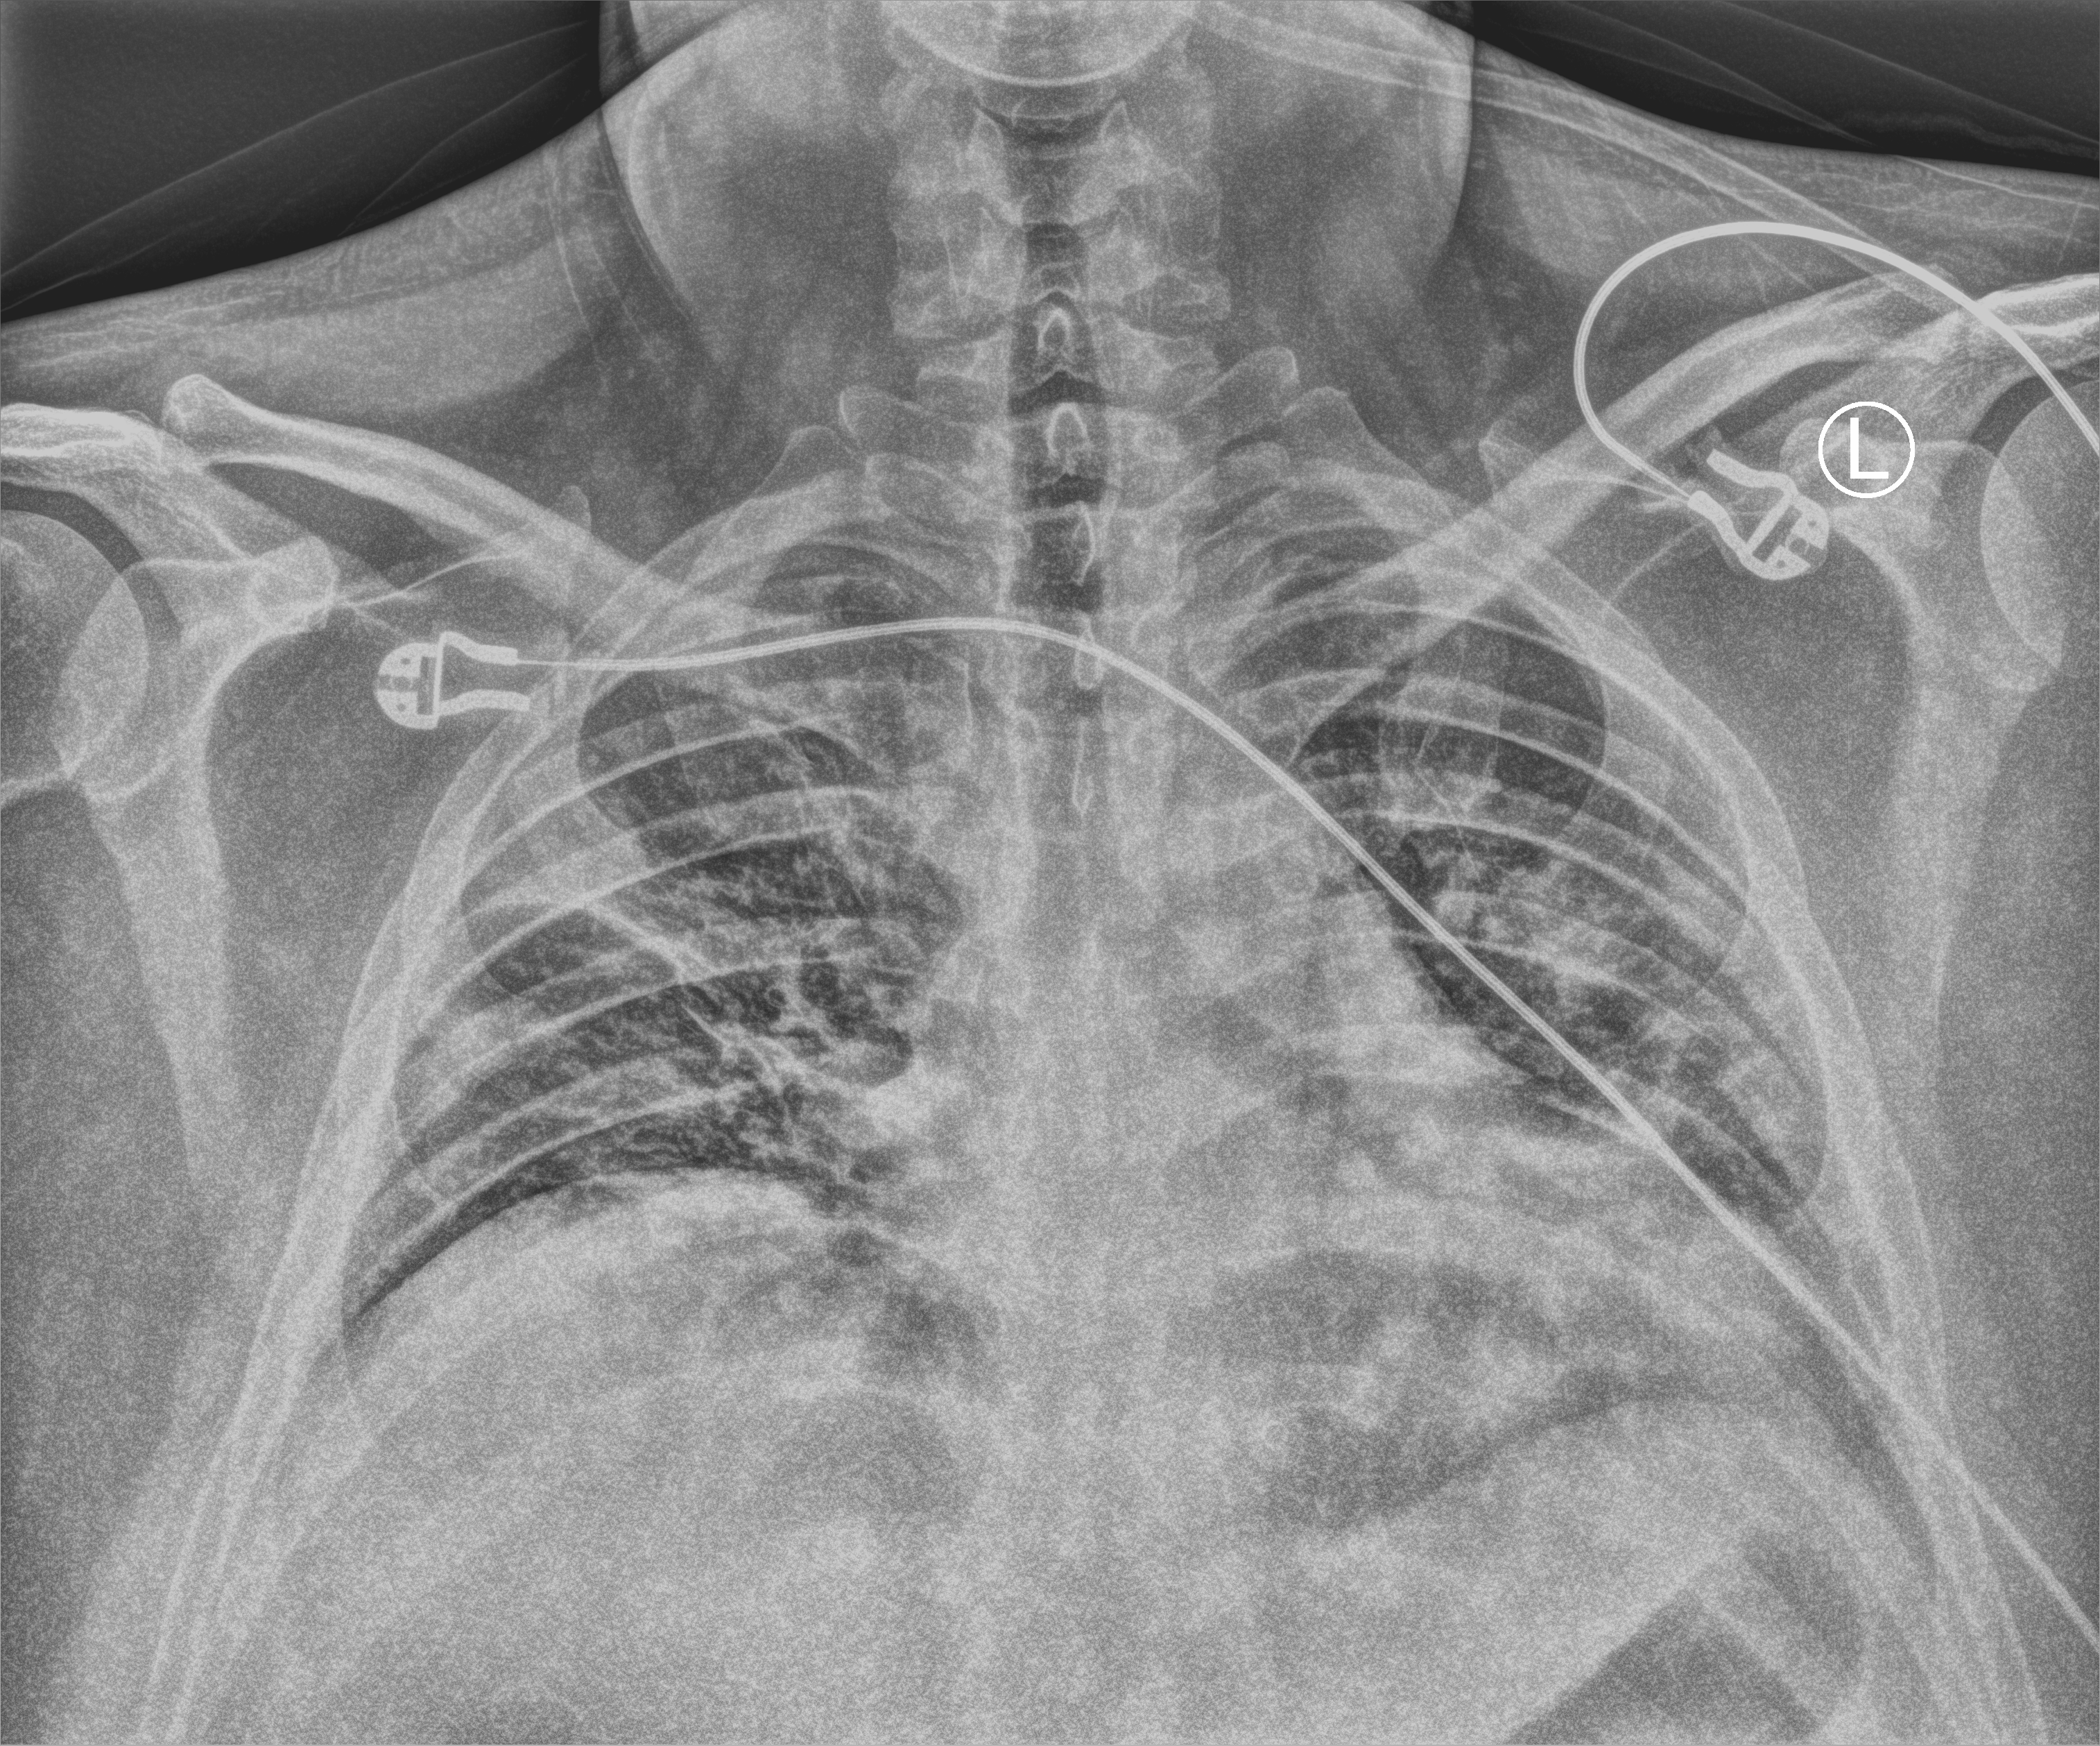
Chest X-ray (portable), anteroposterior (AP) projection. Male patient hospitalised with COVID-19, age 18–59 years.
Admission-level facts for this patient (not findings on this image; timing relative to this image not recorded):
- admitted to intensive care during this hospital stay: no
- mechanically ventilated during this hospital stay: no
- chronic kidney disease (admission record): no